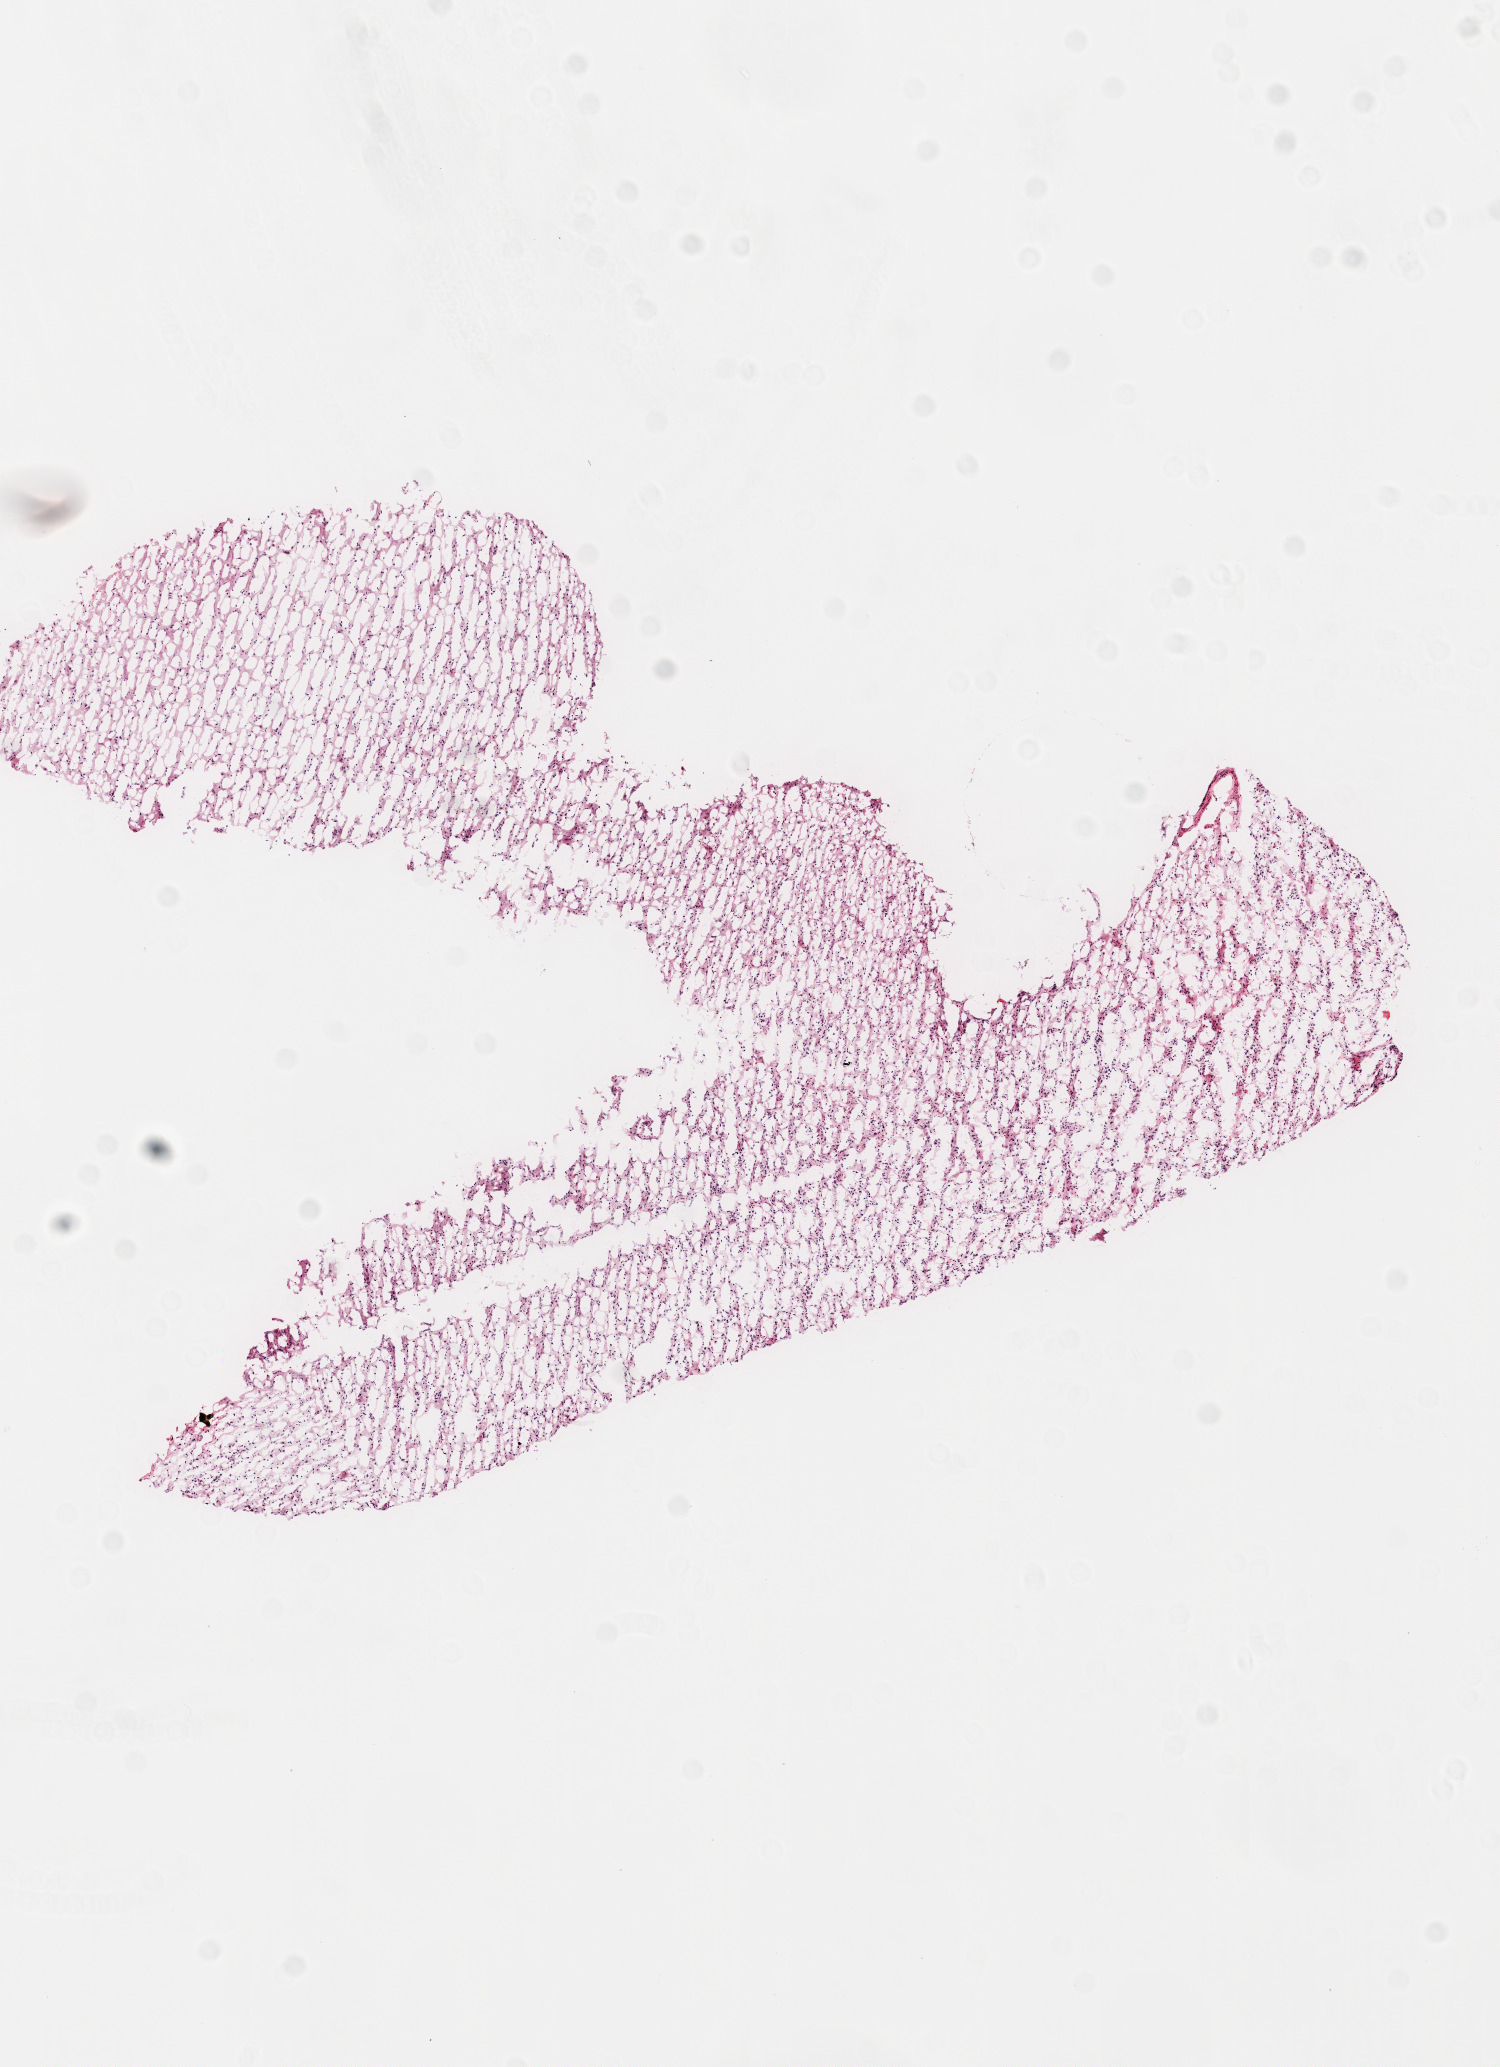
Whole-slide histology image, H&E, a low-resolution overview of the entire scanned area, about 6.0 x 8.3 mm, frozen section from the top of the tissue portion, sample: primary tumour, brain. Female patient; age at initial diagnosis 77 years. Slide review estimates, as recorded: tumour cells 100%, tumour nuclei 100%, normal cells 0%, stromal cells 0%, necrosis 0%.
• histologic diagnosis: Glioblastoma